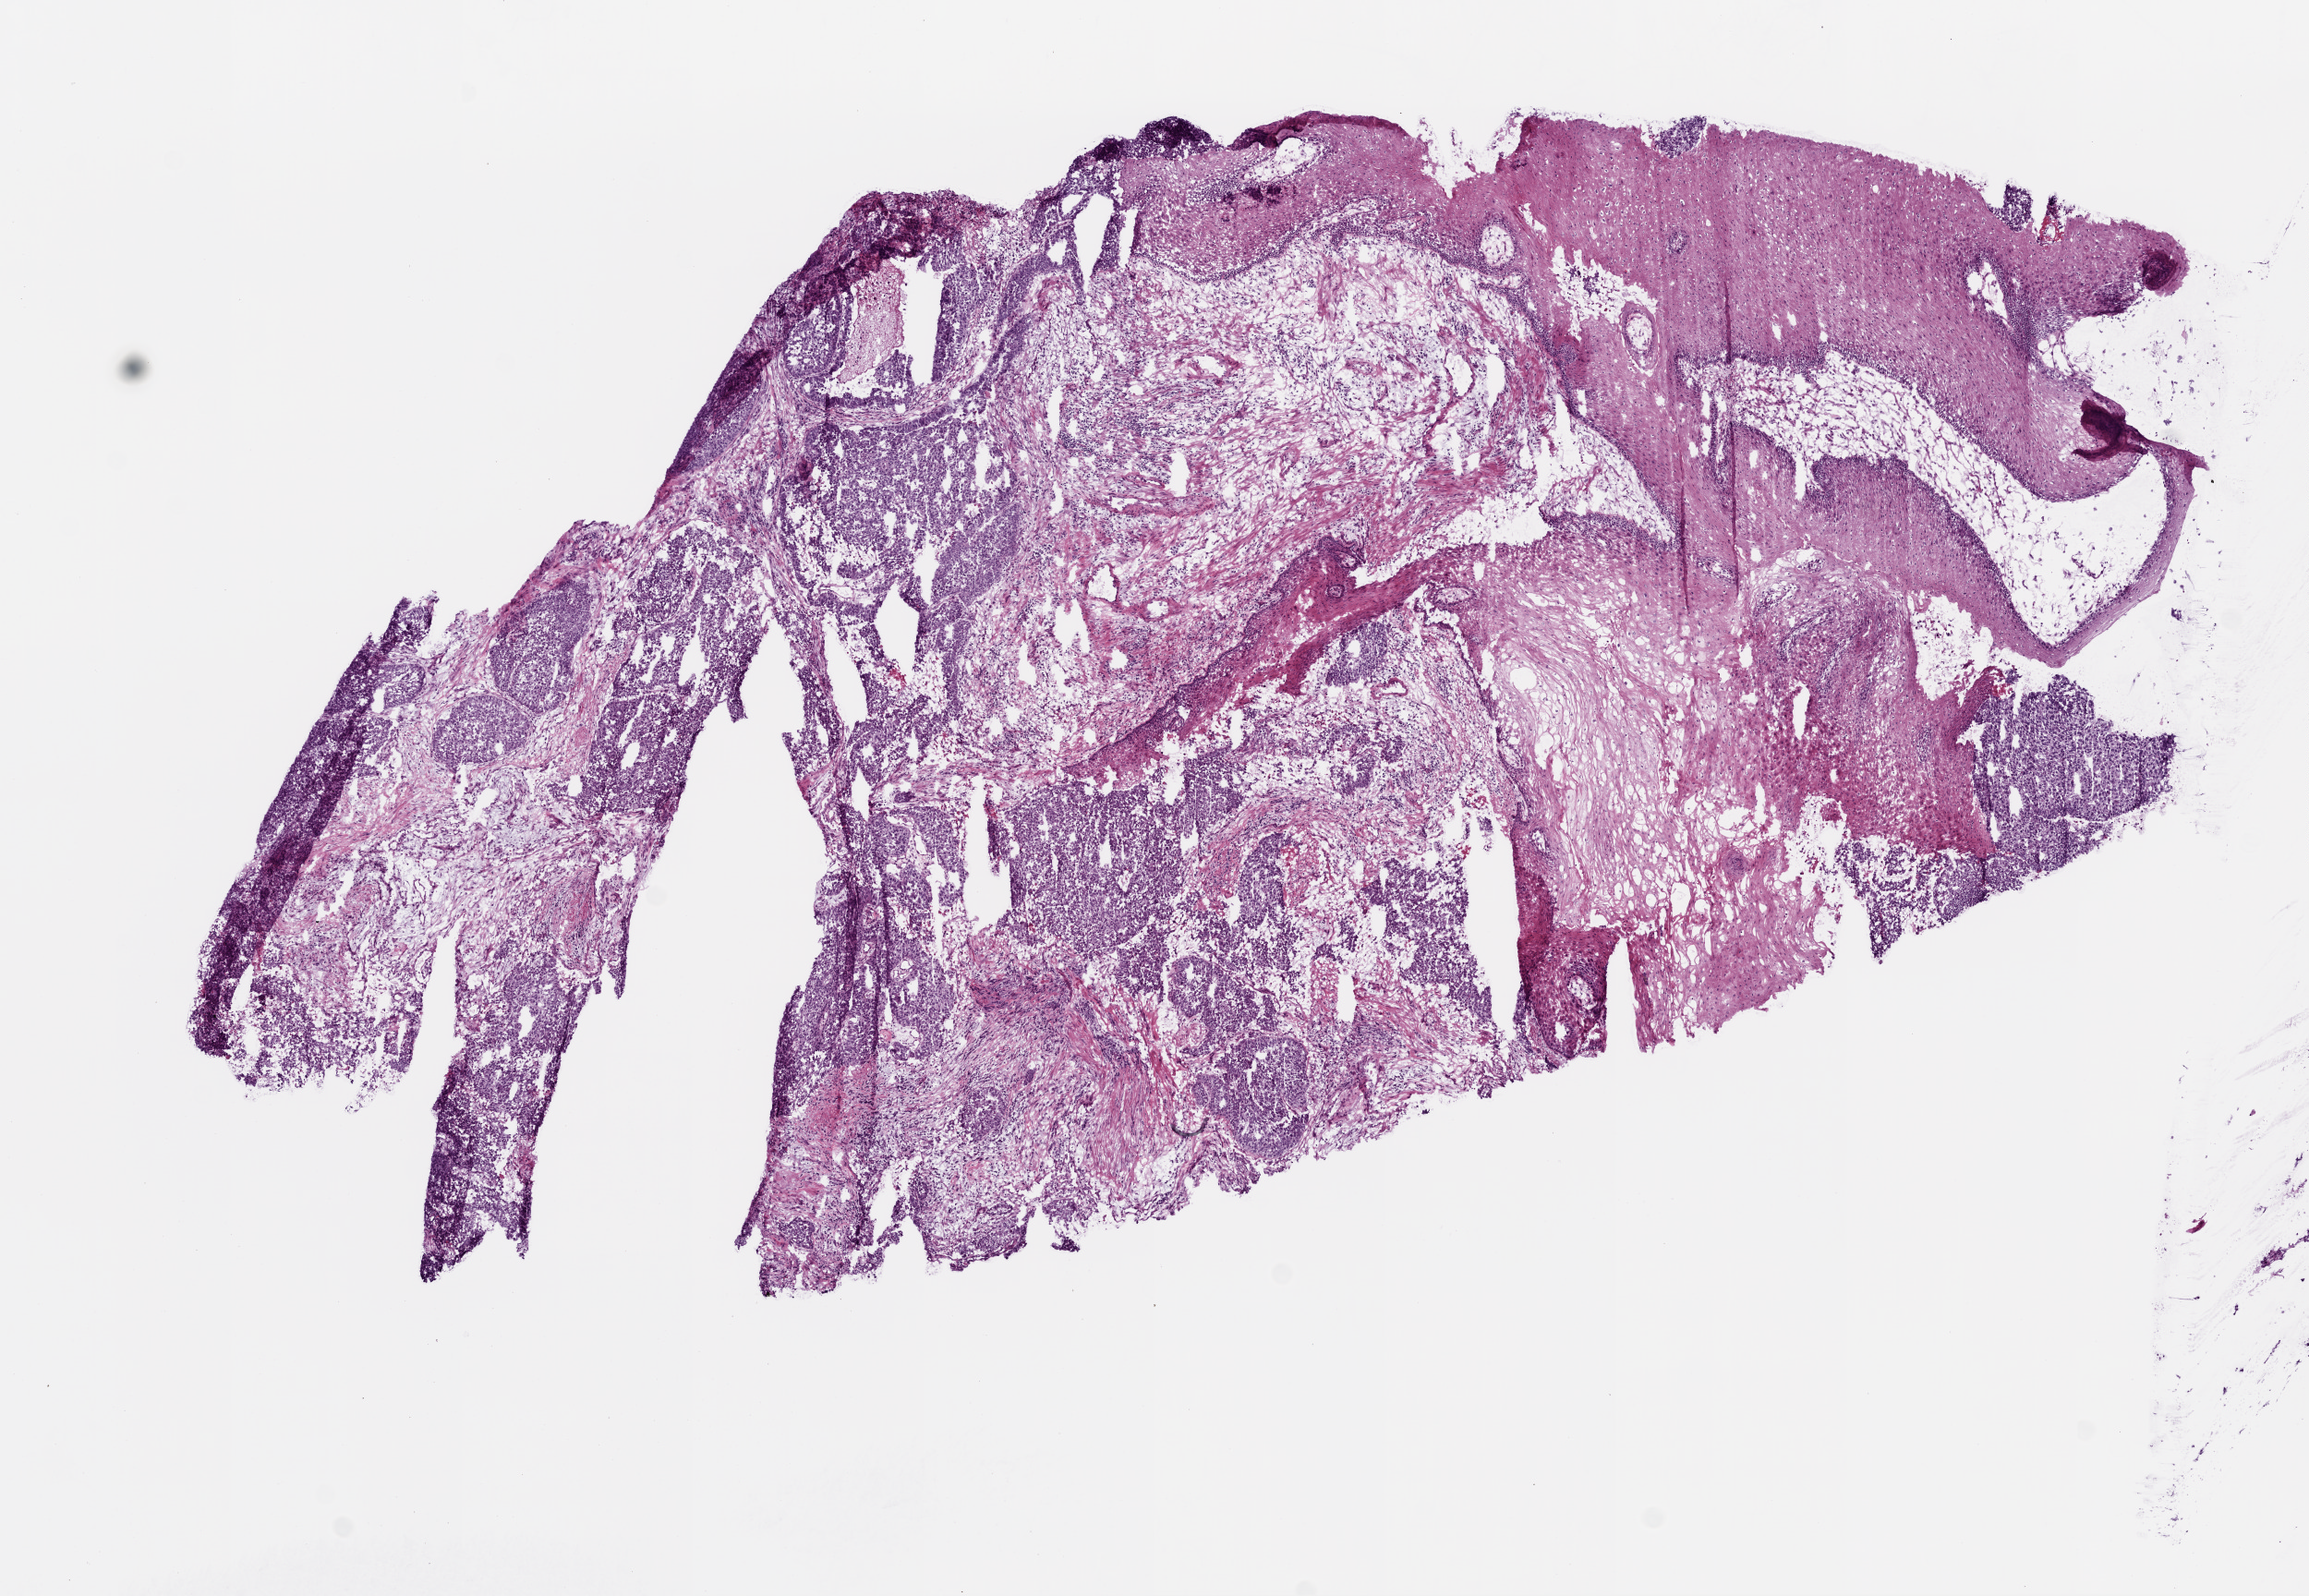
H&E whole-slide image, low-resolution overview of the scanned area, about 10.0 x 6.9 mm (slide scanned at 20x), frozen section from the top of the tissue portion, primary tumour sample from the stomach. Patient: male, age at initial diagnosis 72 years. Histologic grade: G3 (poorly differentiated). Slide review estimates, as recorded: tumour cells 43%, tumour nuclei 75%, normal cells 30%, stromal cells 25%, necrosis 2%.
* lymph nodes positive (case pathology): 0 of 23 examined
* AJCC pathologic stage: IB (5th edition)
* diagnosis: Adenocarcinoma, NOS (cardia, NOS)